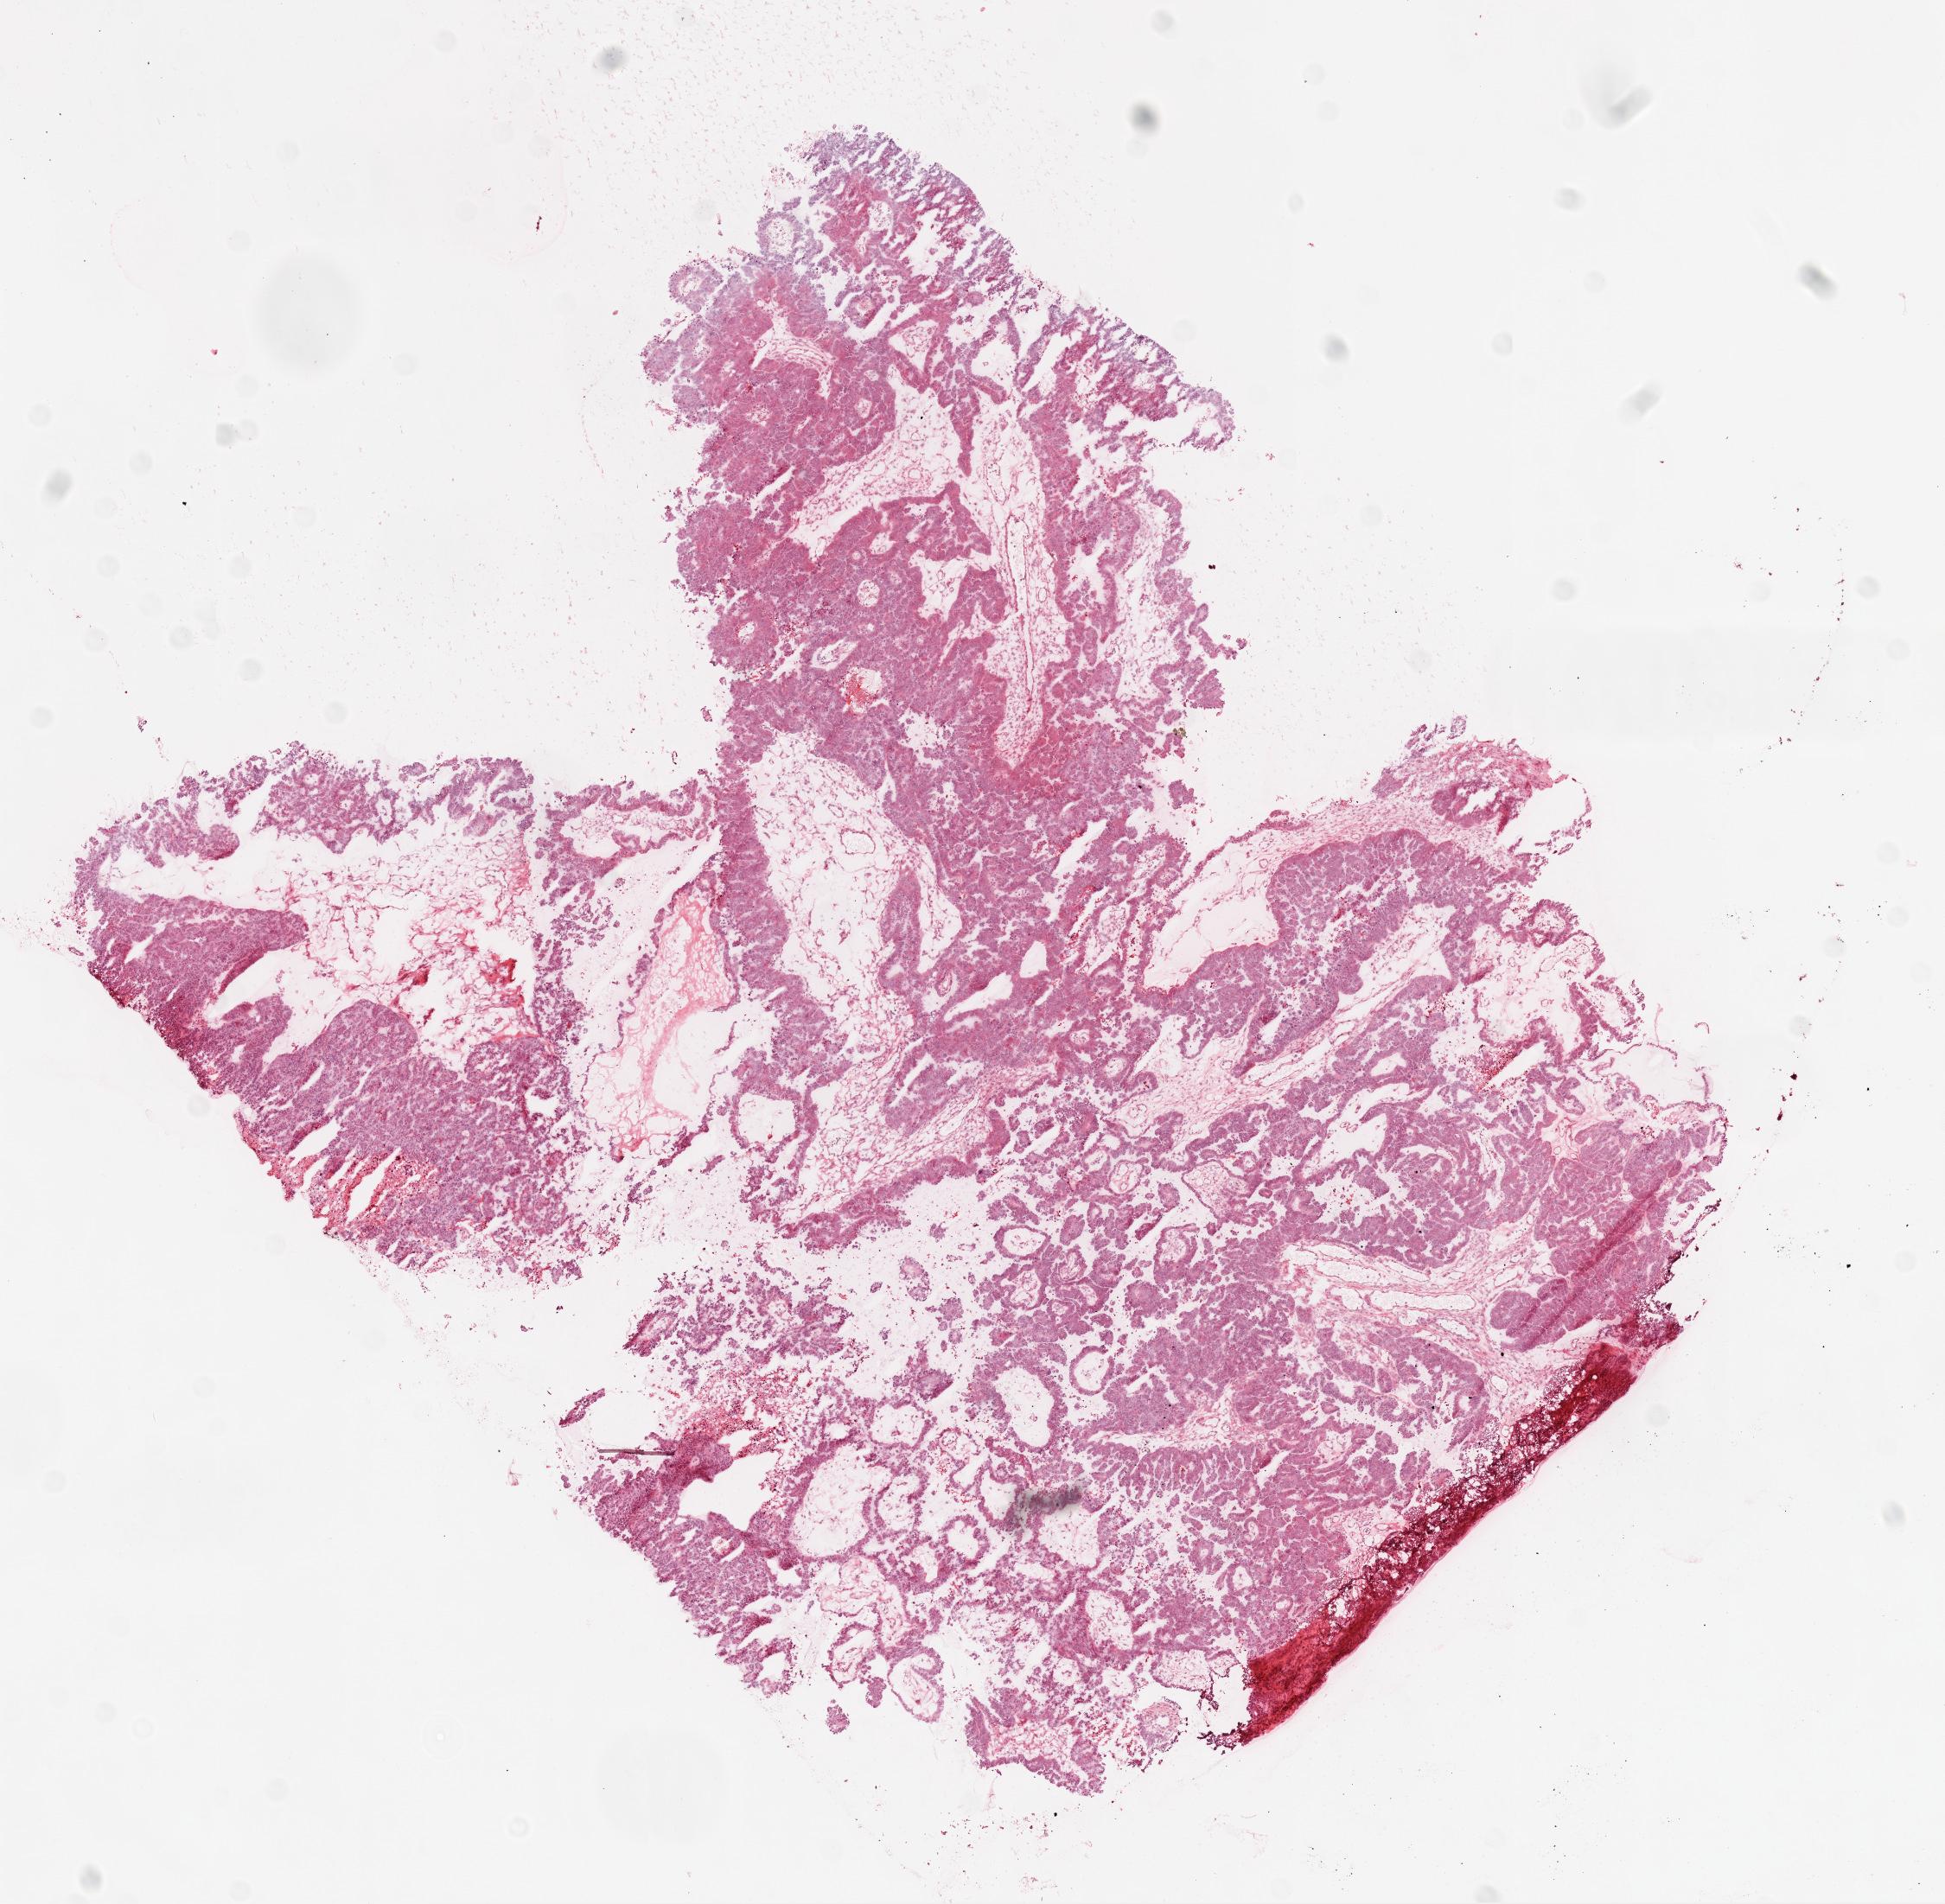
H&E whole-slide image, whole scanned area (about 9.0 x 8.8 mm) shown as a low-resolution overview, frozen section, primary tumour sample from the ovary. Female, age 76 years at initial diagnosis. Histologic grade: G2 (moderately differentiated). Composition of this section per pathologist review: tumour cells 80%, tumour nuclei 85%, normal cells 0%, stromal cells 15%, necrosis 5%.
Histologic diagnosis: Serous cystadenocarcinoma, NOS. FIGO stage: IIIC. Laterality: bilateral.